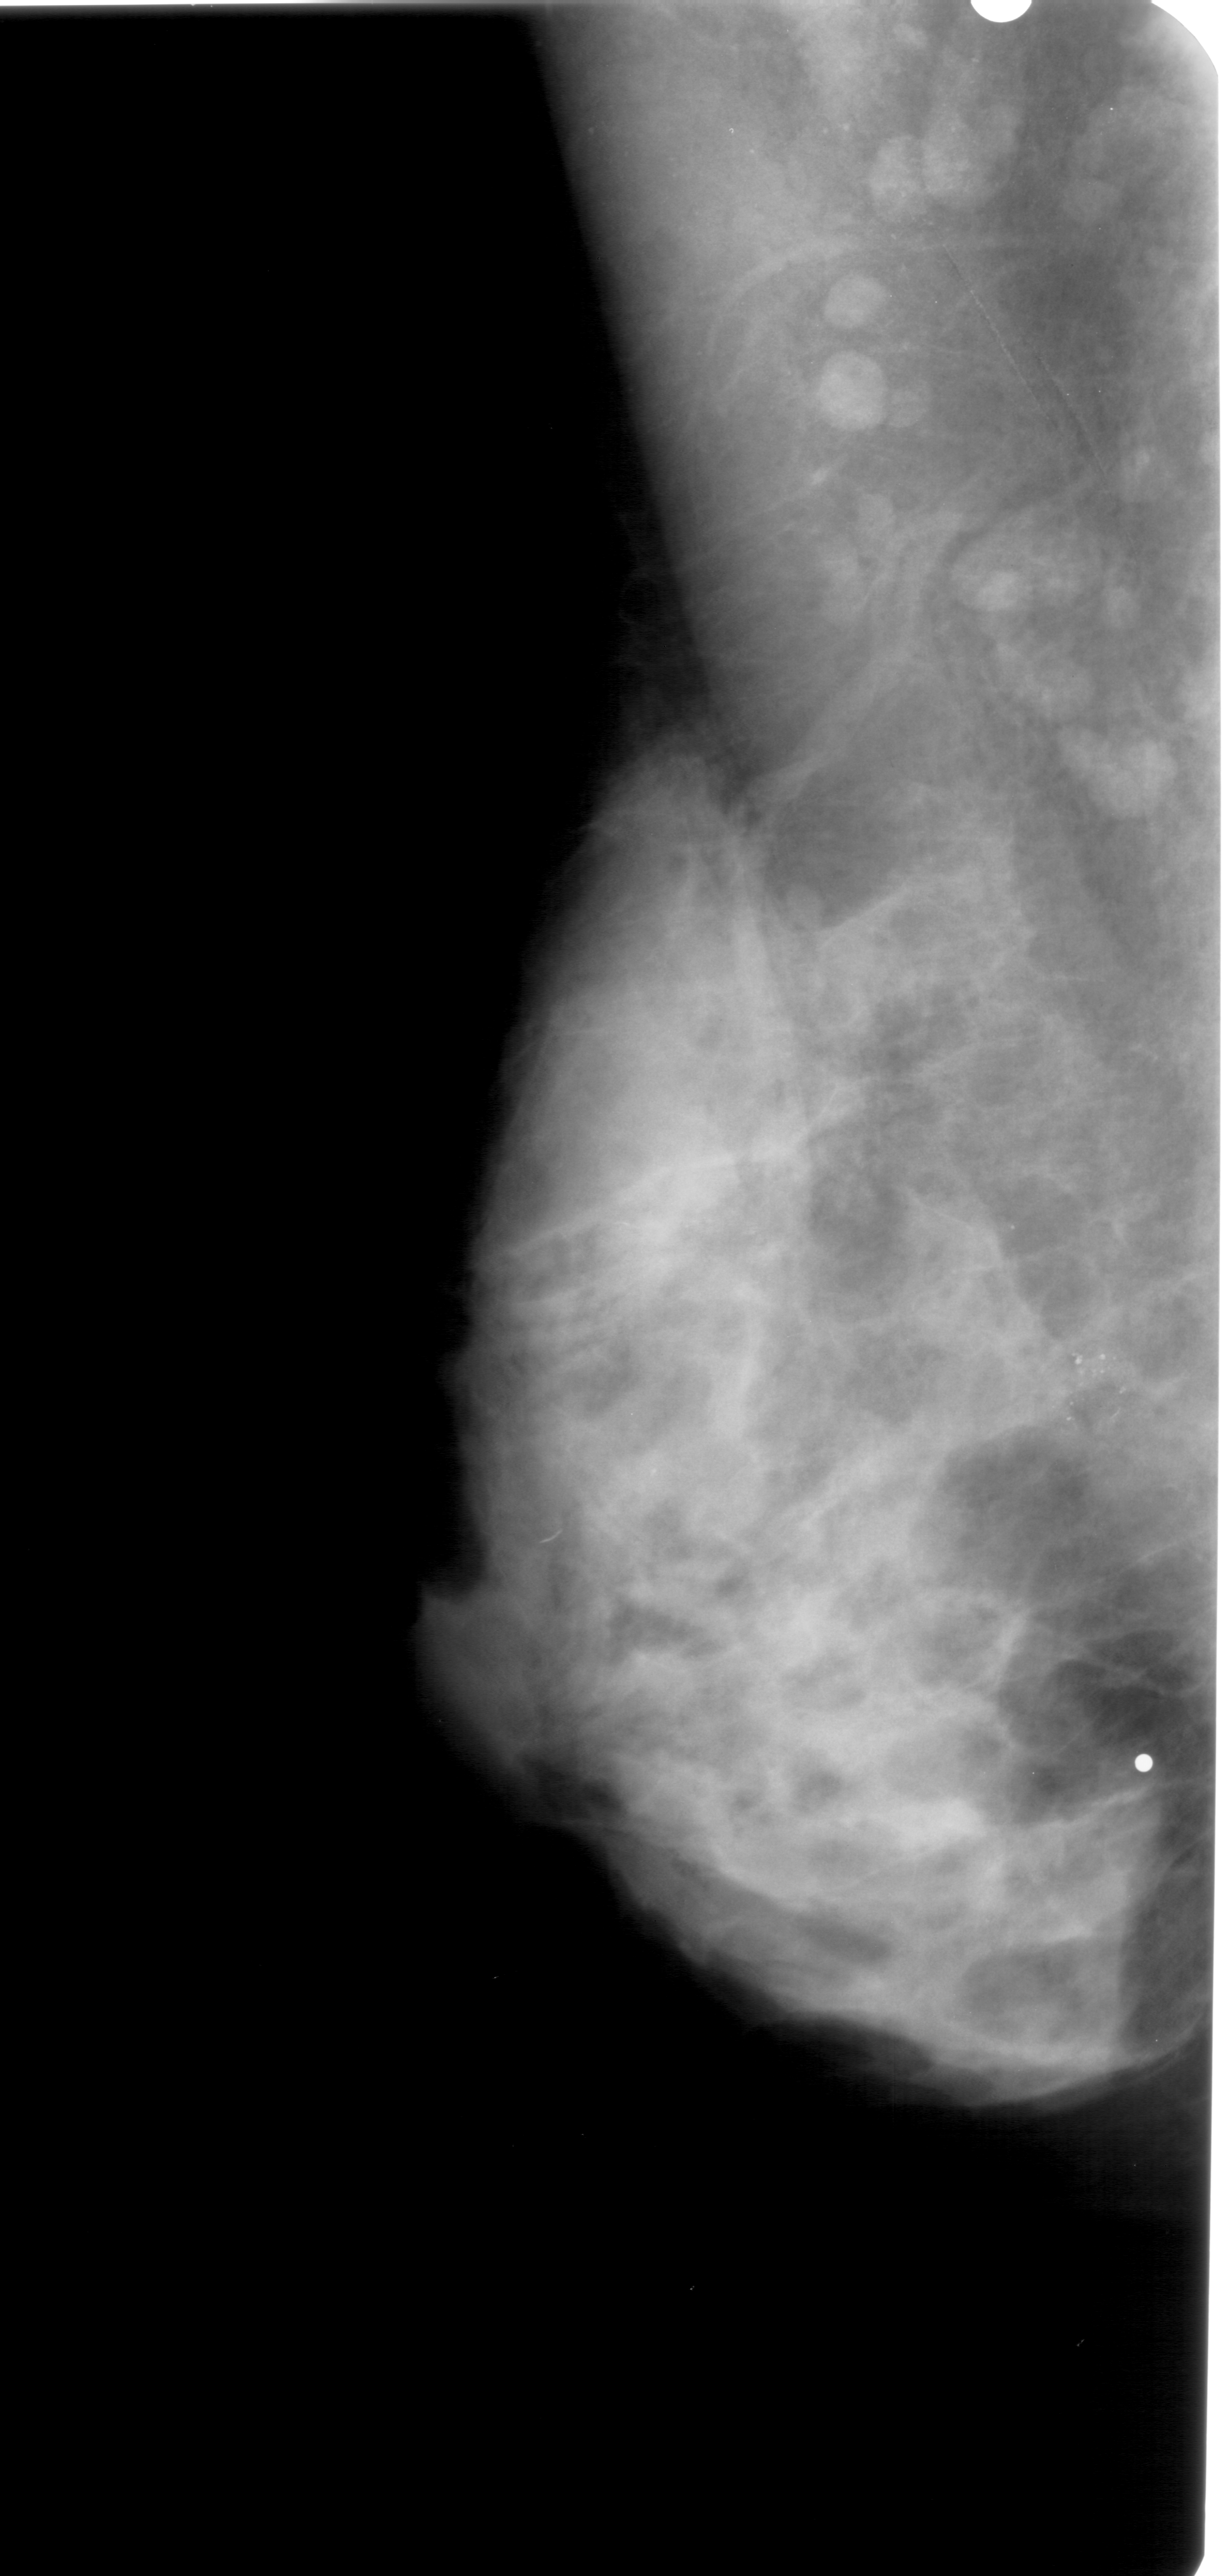
Digitized screen-film mammogram. Left breast. MLO view. Breast composition: extremely dense (BI-RADS density category 4 of 4). 1227 × 2576 image matrix.
Expert-marked regions of interest on this image (one box per marked abnormality):
- calcifications, morphology pleomorphic, distribution clustered; BI-RADS assessment category 4; pathology (as recorded): benign: box from (x=982, y=1274) to (x=1161, y=1512) px